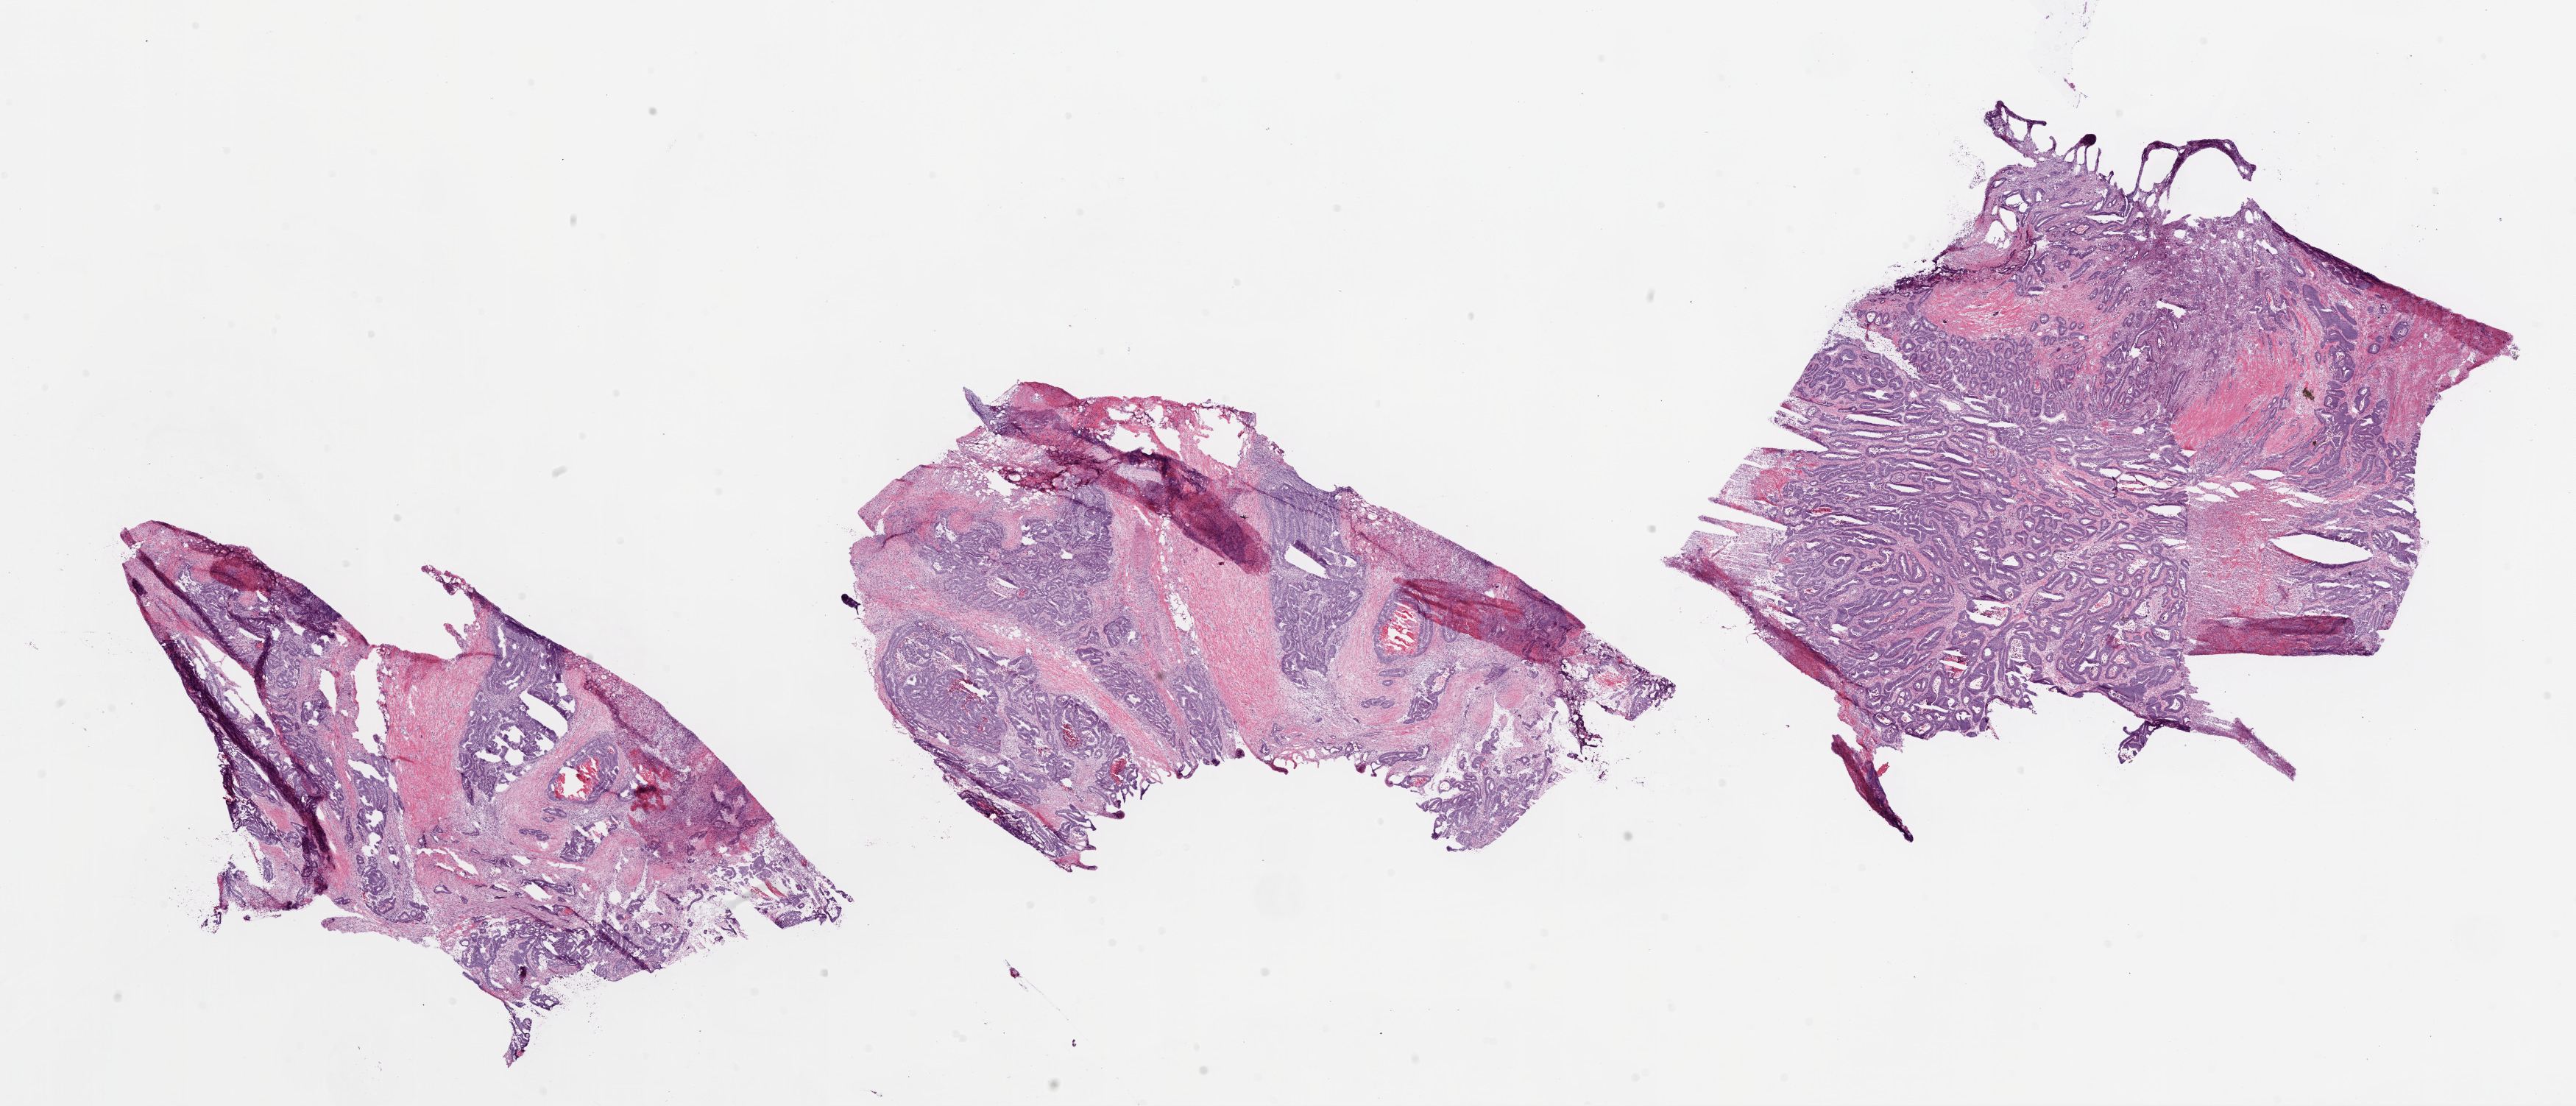
Whole-slide histology image, H&E — shown as a low-resolution overview of the whole scanned area (about 28.1 x 12.1 mm, acquisition: 20x scan), frozen section from the bottom of the tissue portion, sample: primary tumour, colon. Male, age 62 years at initial diagnosis. Pathologist review of this section (percent, as recorded): tumour cells 50%, tumour nuclei 75%, normal cells 35%, stromal cells 5%, necrosis 10%.
Lymph nodes positive (case pathology): 0 of 30 examined. TNM: T3 N0 M0. AJCC pathologic stage: IIA. Pathologic diagnosis: Adenocarcinoma, NOS.